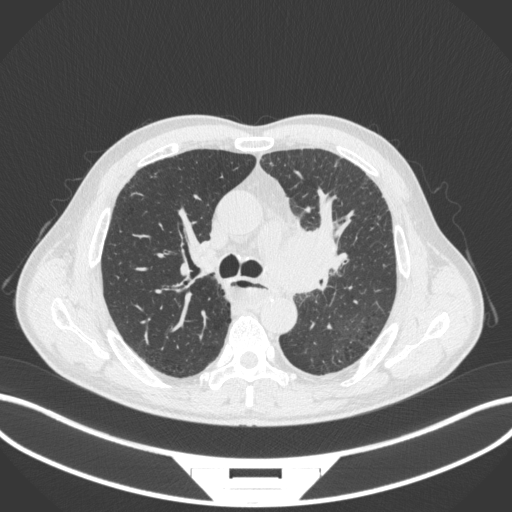
Chest CT, one axial slice. Position 248 of 411 along the scan axis. Reconstruction kernel B31f. 120 kVp. Lung window (W 1500 / L -600 HU). 512 × 512 image matrix. Patient: male, 57 years. Case-level facts recorded for this patient, not image findings: clinical TNM (as recorded): T2a N1 M0.
Outlined on this slice (bounding box drawn by a radiologist):
- lung tumour (recorded histology: squamous cell carcinoma): bounding box (x1, y1, x2, y2) in pixels: (259, 214, 349, 300)